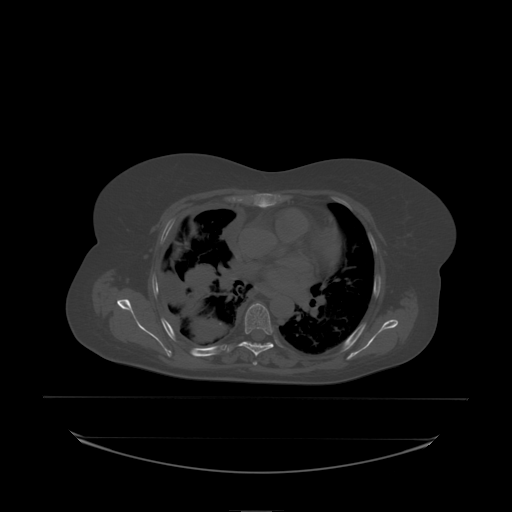
CT including the spine, one axial slice; slice 150 of 242 in the series (ordered by position); bone window (W 1800 / L 400 HU); 512 × 512 image matrix, field of view 500 × 500 mm. Patient: female, 53 years. Case-level facts recorded for this patient, not image findings: primary cancer: lung; vertebrae with lytic lesions (as recorded): T7, L1.
Outlined on this slice (semi-automatic segmentation, software-assisted and operator-edited):
- T6 vertebra: bounding box [x1, y1, x2, y2] px = [245, 304, 273, 335]